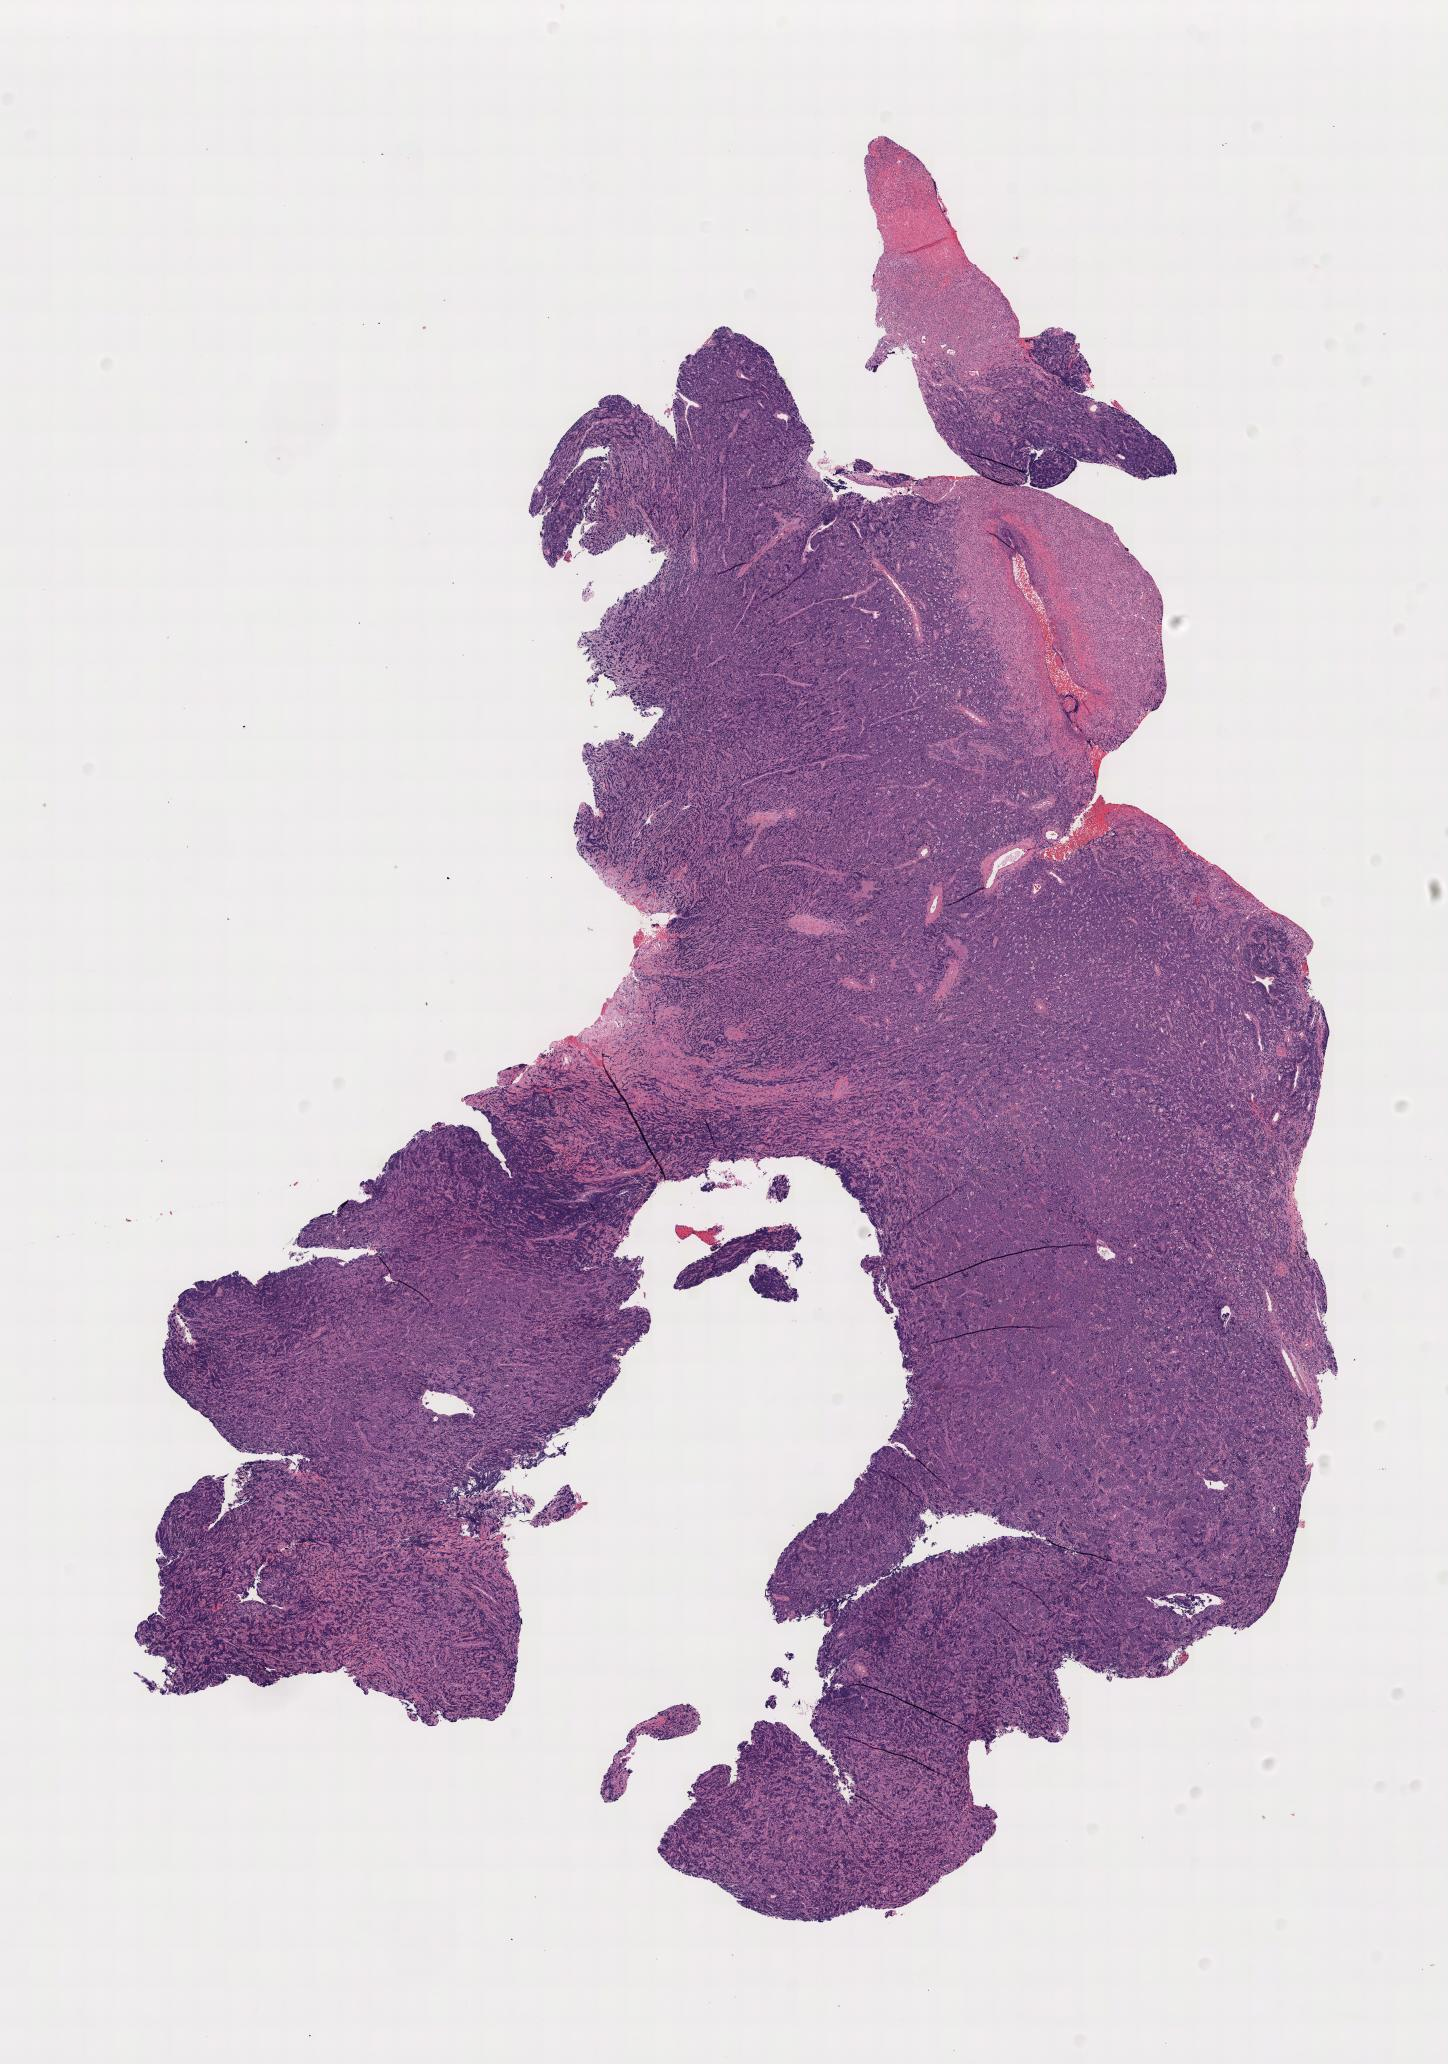
H&E whole-slide image — low-resolution overview of the scanned area, tumor tissue, site: mouth. Patient: female, age at initial diagnosis 7 years.
Diagnosis: Diffuse large B-cell lymphoma, NOS.